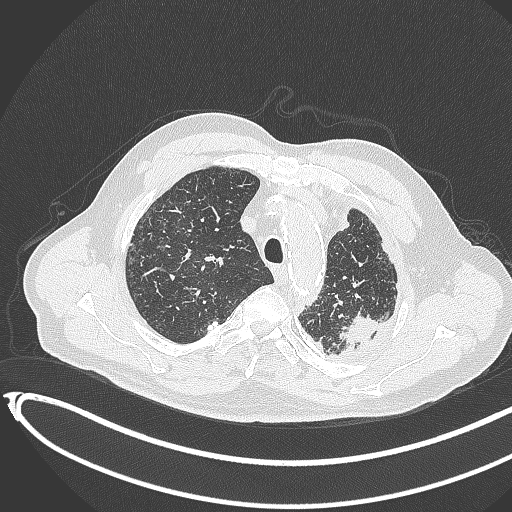
Chest CT, one axial slice; 120 kVp; lung window (W 1500 / L -600 HU); 1 mm slice thickness; 512 × 512 image matrix. Male patient, age 78 years. Case-level facts recorded for this patient, not image findings: clinical TNM (as recorded): T1c N0 M1.
Annotated regions visible in this slice (rectangle marked by the reading radiologist):
- lung tumour (recorded histology: adenocarcinoma): box from (x=337, y=307) to (x=383, y=344) px